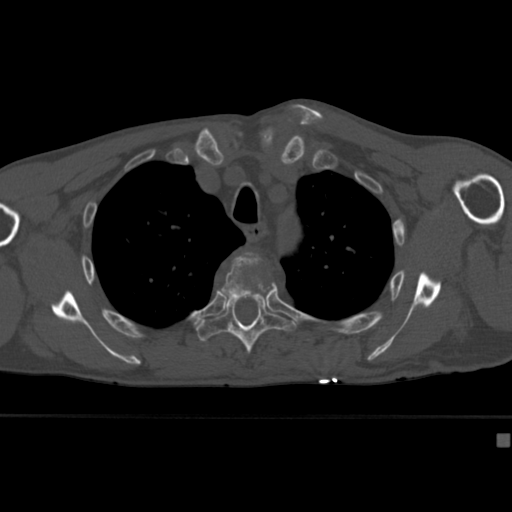
CT including the spine, one axial slice. 120 kVp. Bone window (W 1800 / L 400 HU). 512 × 512 image matrix, field of view 337 × 337 mm. Male patient, age 64 years. Case-level facts recorded for this patient, not image findings: primary cancer: uterus; vertebrae with lytic lesions (as recorded): T1, T4, T5, T7, L5.
Structures marked on this image (semi-automatically segmented with operator editing):
- T4 vertebra: bounding box [x1, y1, x2, y2] px = [221, 253, 273, 303]
- T5 vertebra: [196, 293, 297, 355]